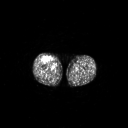
FDG PET of an extremity soft-tissue mass (from a PET/CT study), one axial slice; slice 254 of 311 in the series (ordered by position); 3.27 mm slice thickness; 128 × 128 image matrix, field of view 700 × 700 mm. Male patient, age 56 years. Case-level facts recorded for this patient, not image findings: histological type: pleiomorphic leiomyosarcoma; grade: intermediate; site of the primary tumour: right thigh.
Outlined on this slice (expert contour drawn on MRI and transferred to this co-registered scan by the dataset authors):
- gross tumour volume including surrounding oedema: bounding box (x1, y1, x2, y2) in pixels: (43, 56, 51, 62)